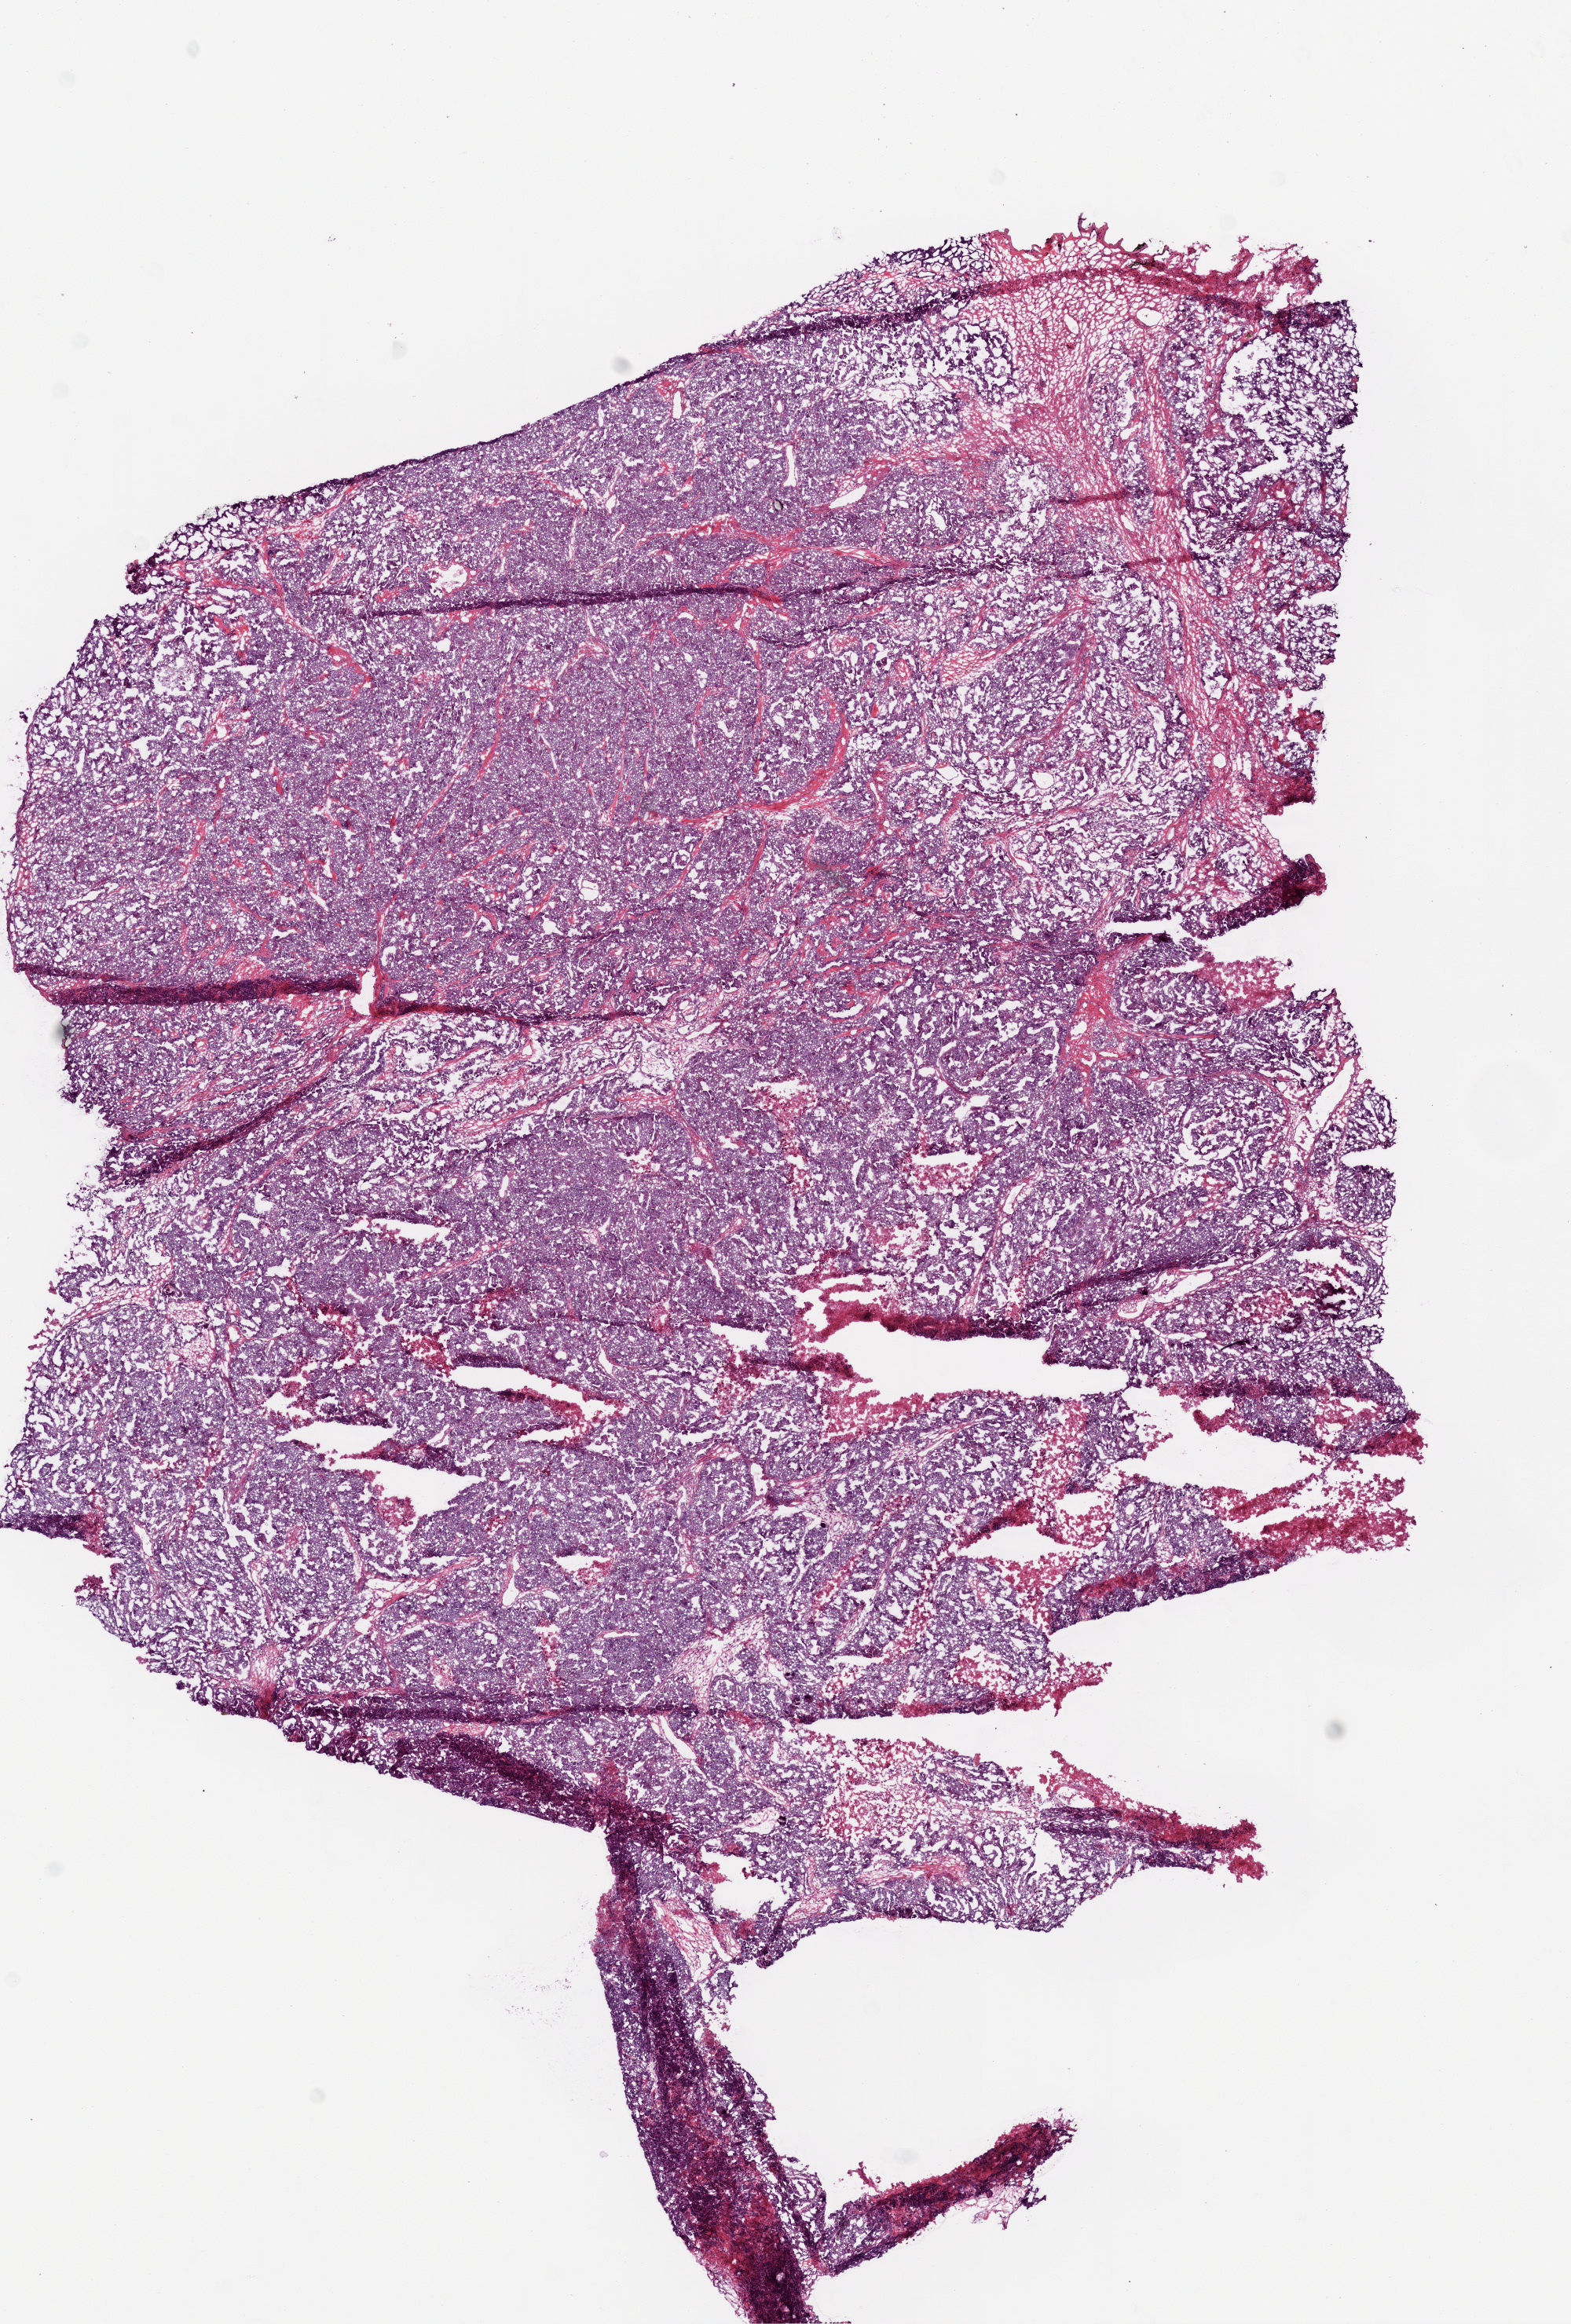
Digitized Hematoxylin and eosin (H&E) stained tissue section (whole slide), shown as a low-resolution overview of the whole scanned area (about 8.0 x 11.9 mm, slide scanned at 20x). Frozen section from the bottom of the tissue portion. Sample: primary tumour, ovary. Patient: female, age at initial diagnosis 79 years. Histologic grade: G3 (poorly differentiated). Composition of this section per pathologist review: tumour cells 95%, tumour nuclei 99%, normal cells 0%, stromal cells 5%, necrosis 0%.
* pathologic diagnosis: Serous cystadenocarcinoma, NOS
* FIGO stage: IIIC
* laterality: bilateral